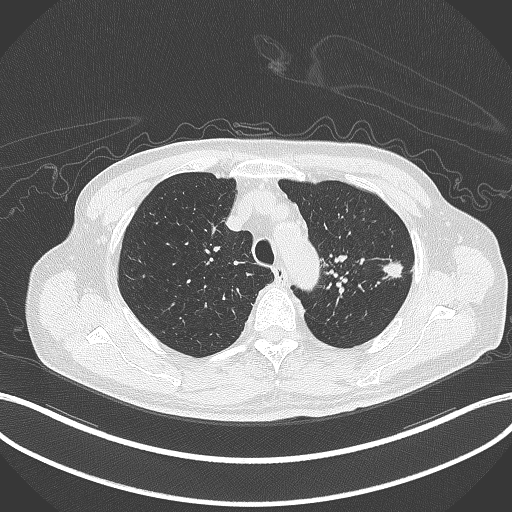
Chest CT, one axial slice; slice 347 of 417 in the series (ordered by position); 120 kVp; lung window (W 1500 / L -600 HU); 1 mm slice thickness; 512 × 512 image matrix, field of view 400 × 400 mm. Patient: male, 77 years. Case-level facts recorded for this patient, not image findings: clinical TNM (as recorded): T3 N1 M0.
Outlined on this slice (rectangle marked by the reading radiologist):
- lung tumour (recorded histology: adenocarcinoma): box from (x=381, y=259) to (x=406, y=281) px